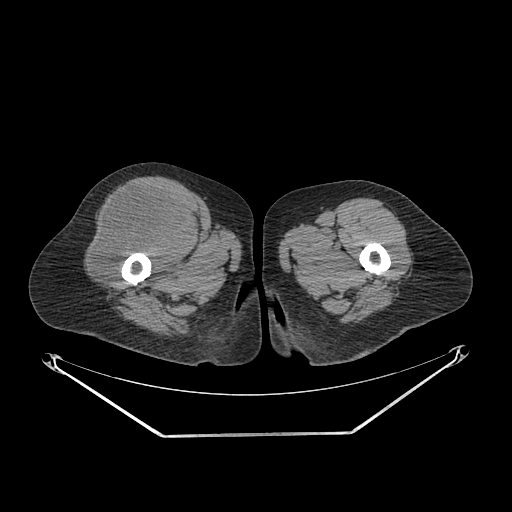
CT of an extremity soft-tissue mass (from a PET/CT study), one axial slice. Position 264 of 311 along the scan axis. Reconstruction kernel SOFT. 140 kVp. Soft-tissue window (W 400 / L 40 HU). 3.75 mm slice thickness. 512 × 512 image matrix, field of view 500 × 500 mm. Female patient. From the clinical record (not read from this slice): histological type: pleiomorphic undifferentiated sarcoma; grade: high; site of the primary tumour: right quadricep.
Structures marked on this image (expert contour drawn on MRI and transferred to this co-registered scan by the dataset authors):
- tumour plus oedema (research contour): bounding box <91,187,191,280> (left, top, right, bottom; pixels)
- tumour (research contour): <91,187,191,280>